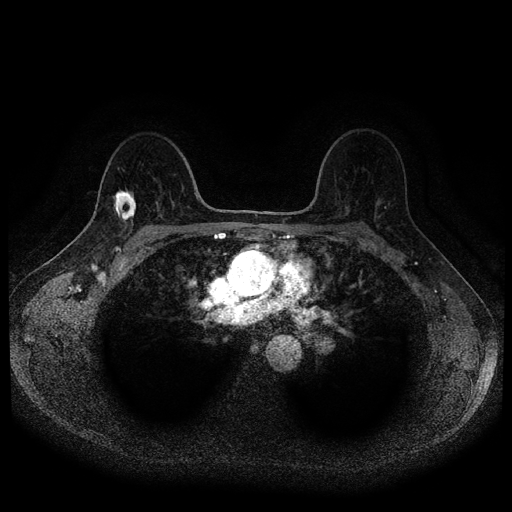
Breast MRI (dynamic contrast-enhanced, multi-phase), one axial slice. Position 69 of 116 along the scan axis. Dynamic contrast-enhanced series, time point 2 of 5 at this slice position (early post-contrast). 1.5 T. TE 2.6 ms, TR 5.4 ms. 2 mm slice thickness. 512 × 512 image matrix, field of view 340 × 340 mm. Patient: female, 49 years.
Outlined on this slice (semi-automatic segmentation, software-assisted and operator-edited):
- breast lesion (labelled 'tumour' in the annotation; benign lesions carry a separate 'benign' label): box from (x=113, y=189) to (x=136, y=226) px